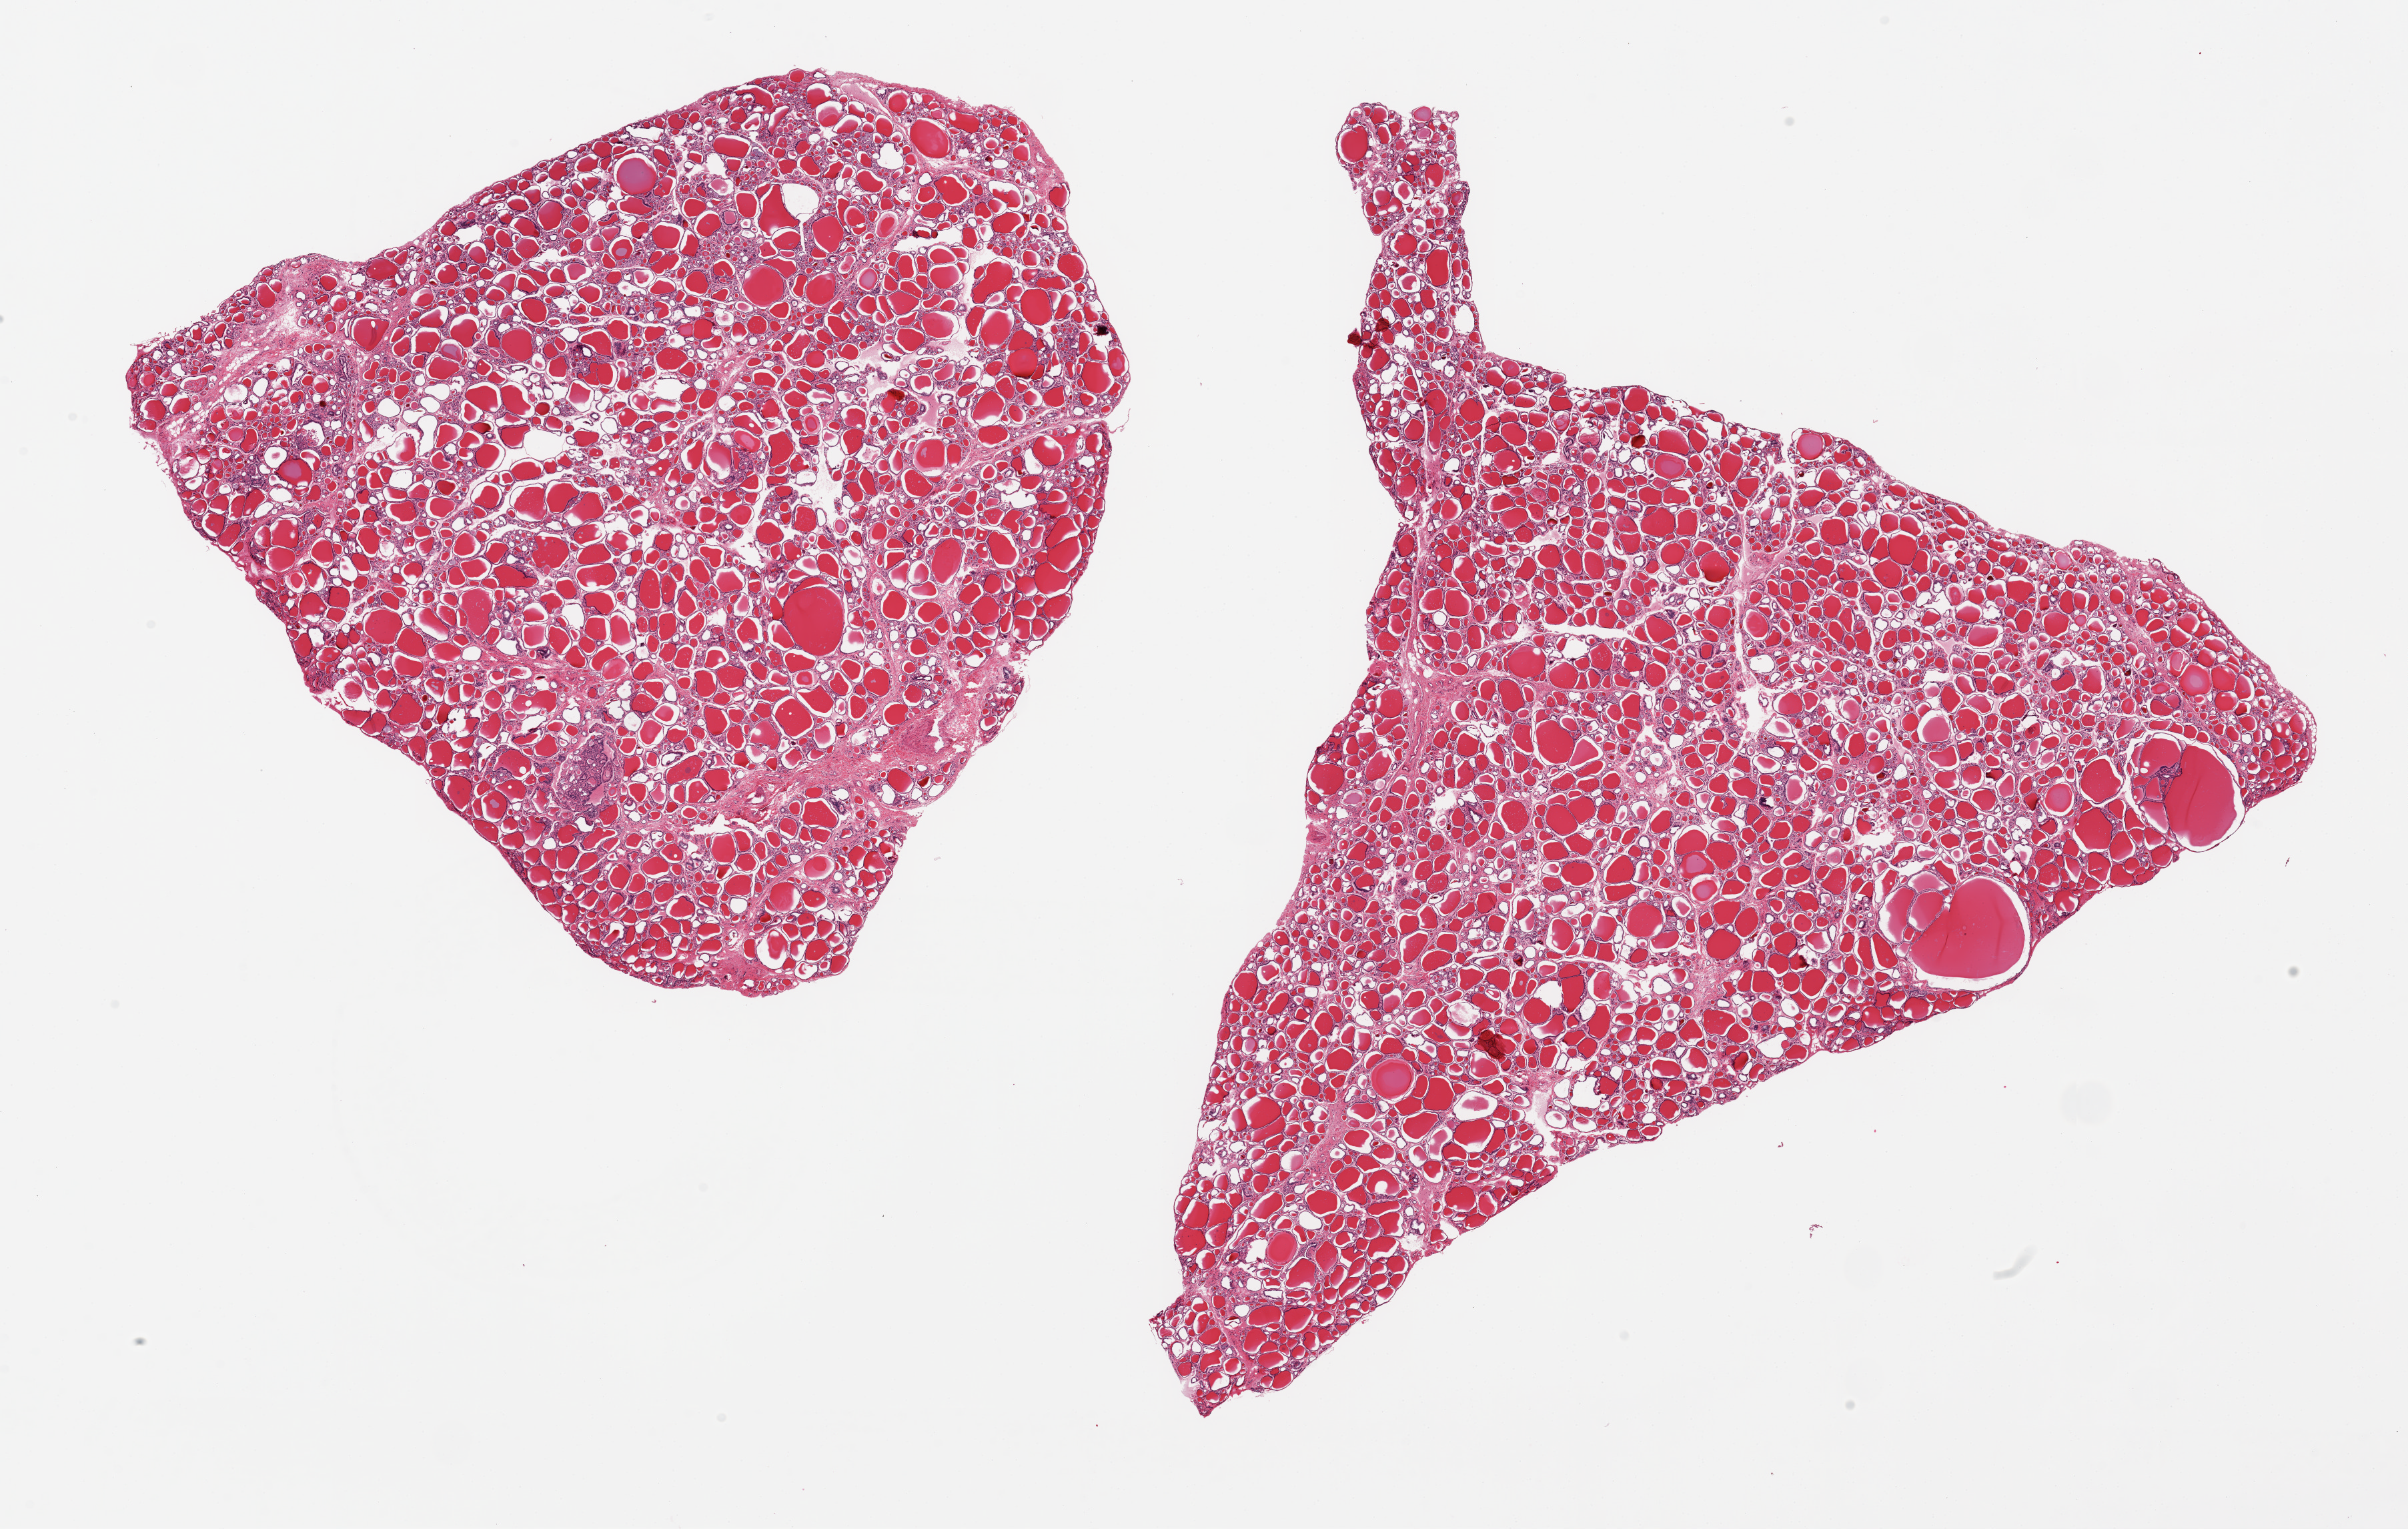
Whole-slide image, H&E stain, a low-resolution overview of the entire scanned area, about 28.5 x 18.1 mm; PAXgene-fixed, paraffin-embedded tissue; section of thyroid (target tissue); tissue donor sample. Donor: female.
Reviewer comment on this tissue sample: 2 pieces, 11x11 & 16x13mm.